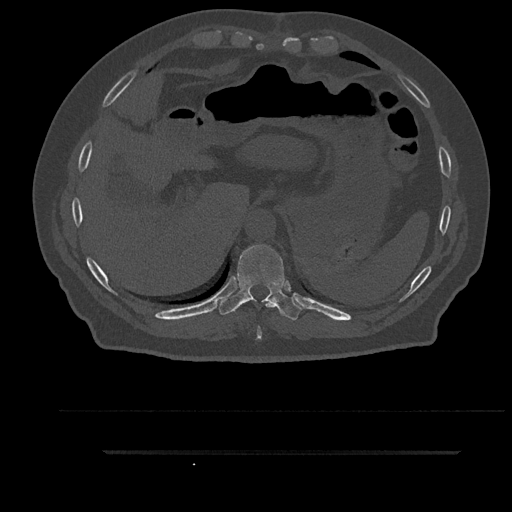
CT including the spine, one axial slice; position 382 of 797 along the scan axis; 120 kVp; bone window (W 1800 / L 400 HU); 512 × 512 image matrix. Patient: male, 63 years. From the clinical record (not read from this slice): primary cancer: renal; vertebrae with lytic lesions (as recorded): T8.
Annotated regions visible in this slice (semi-automatically segmented with operator editing):
- T10 vertebra: bounding box <219,244,303,321> (left, top, right, bottom; pixels)
- T9 vertebra: <256,301,274,340>